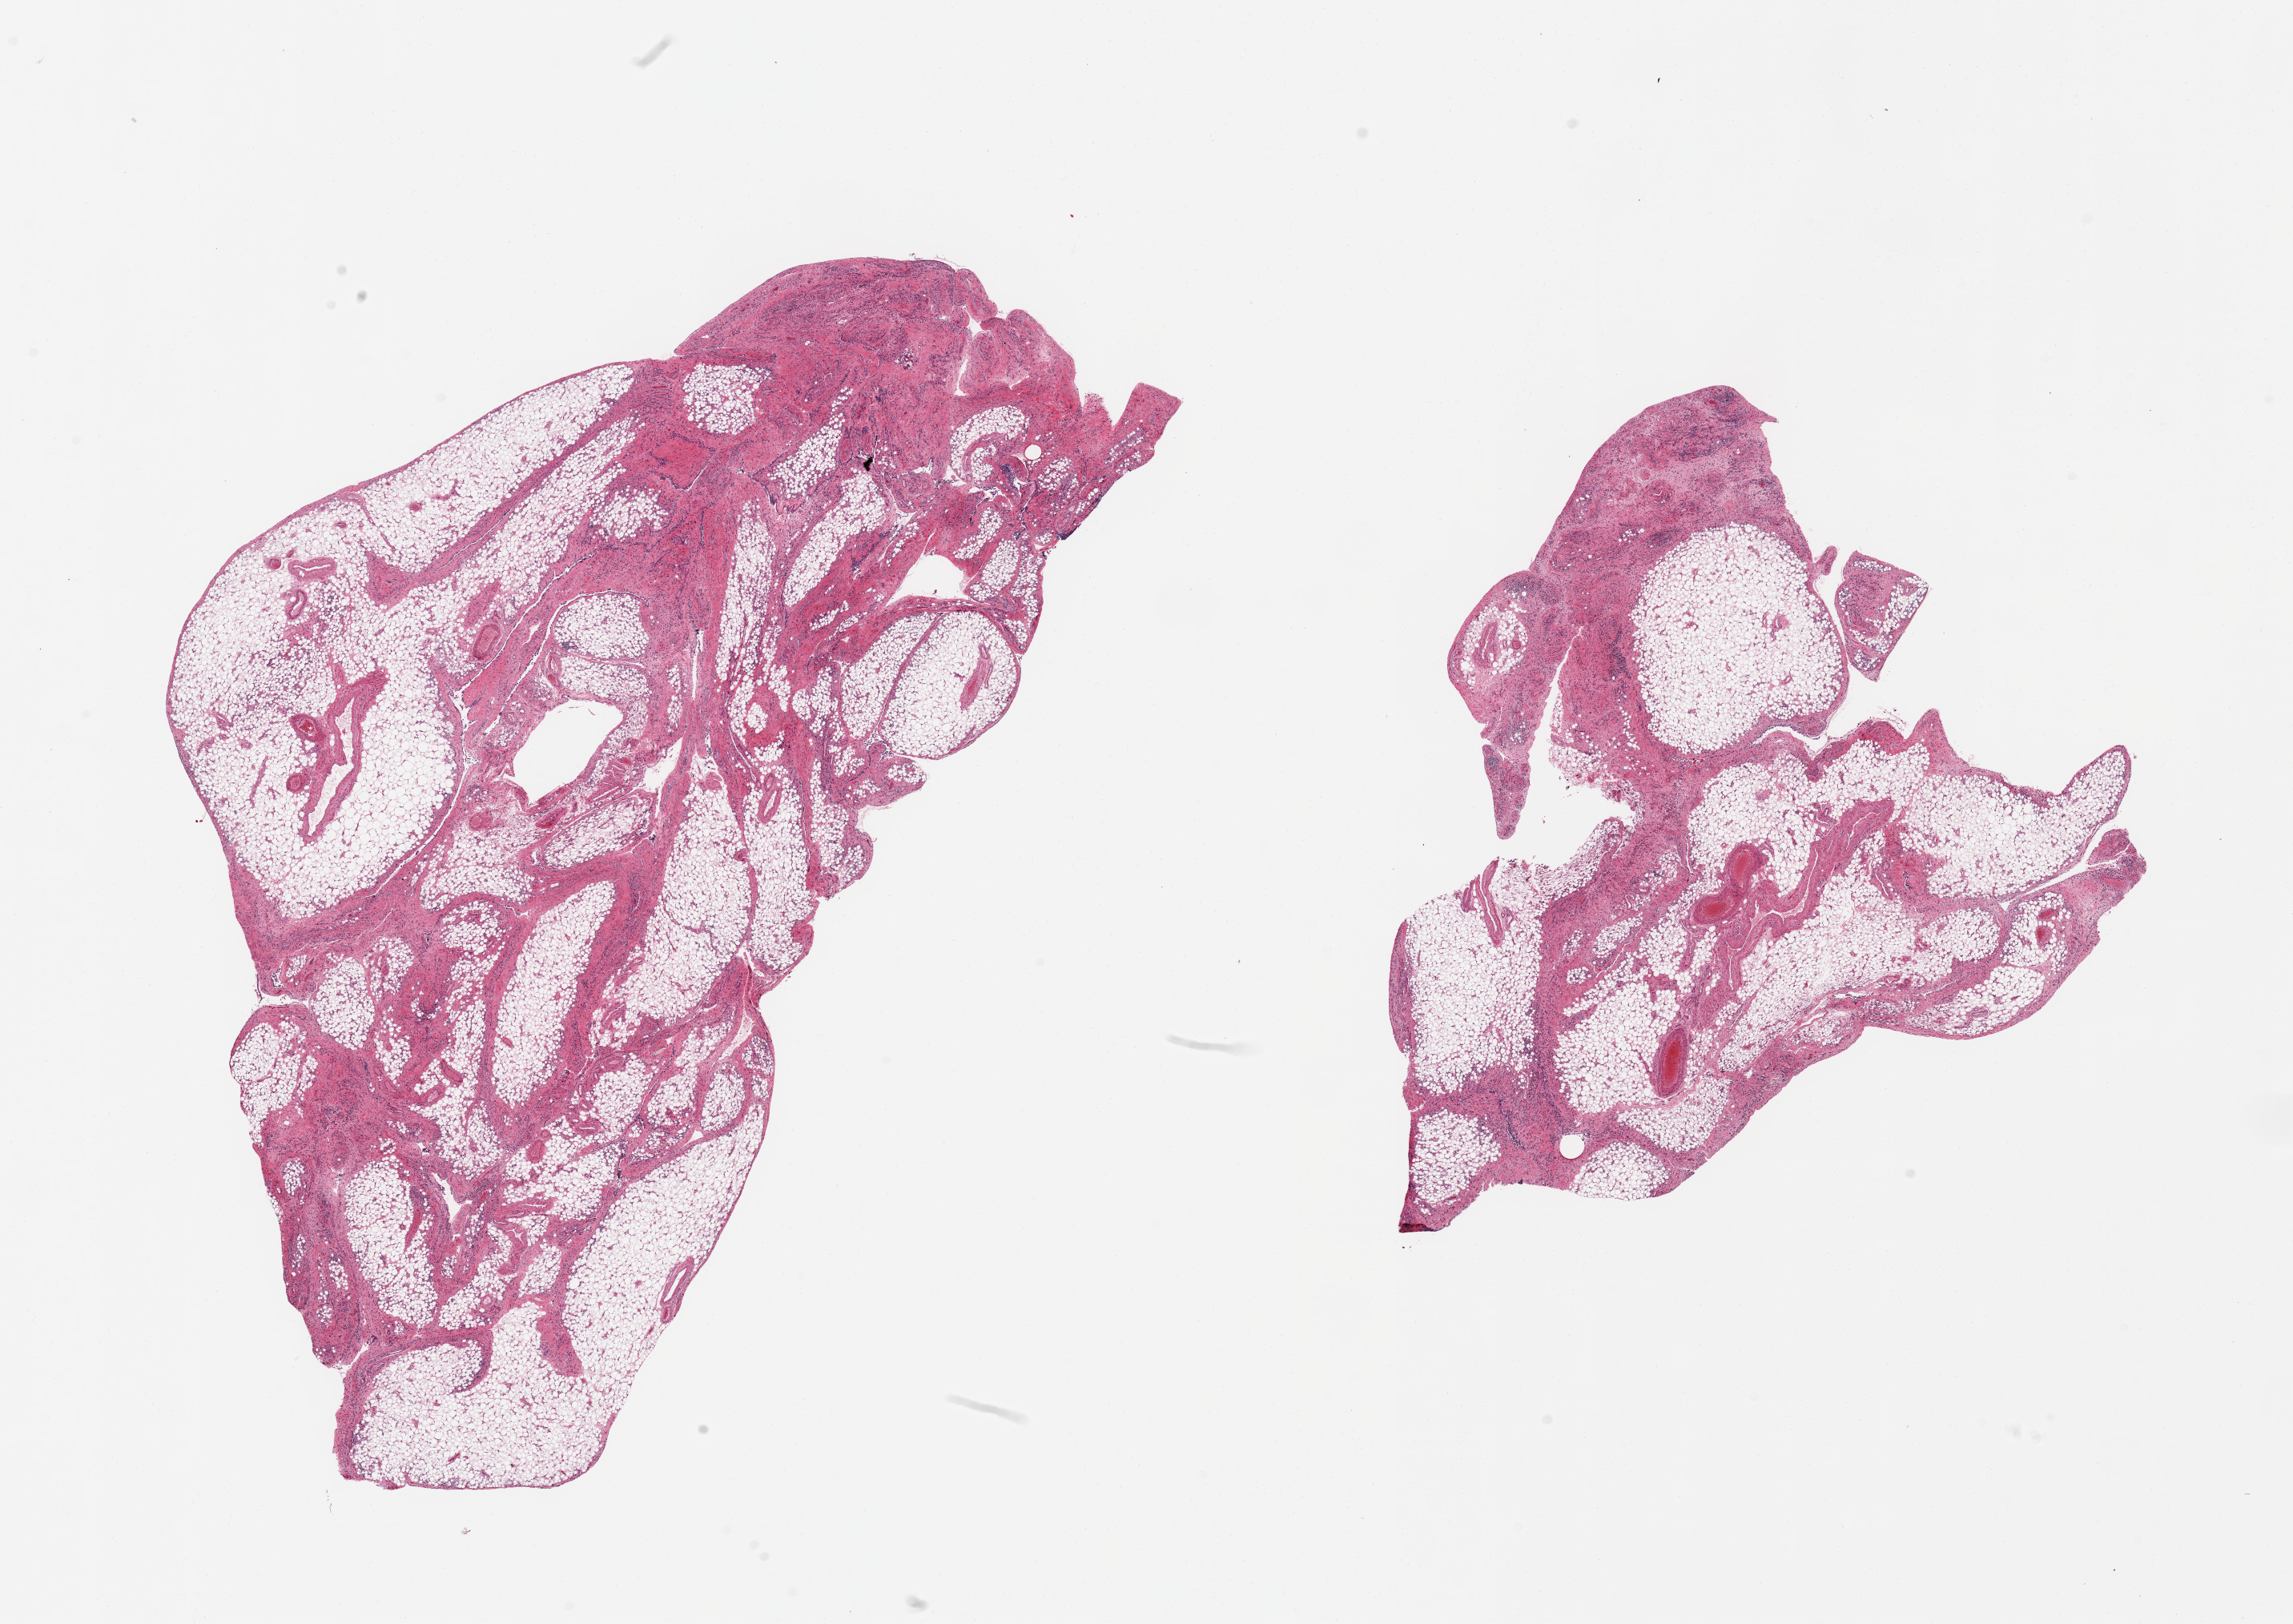
H&E whole-slide image, whole scanned area (about 22.6 x 16.0 mm) shown as a low-resolution overview. PAXgene-fixed paraffin-embedded (PFPE) section. Target tissue: omentum. Donor tissue sample. Donor sex: female.
Pathologist's review note for this sample: 2 pieces, ~50% fascia/mesothelial hyperplasia/vascular elements.